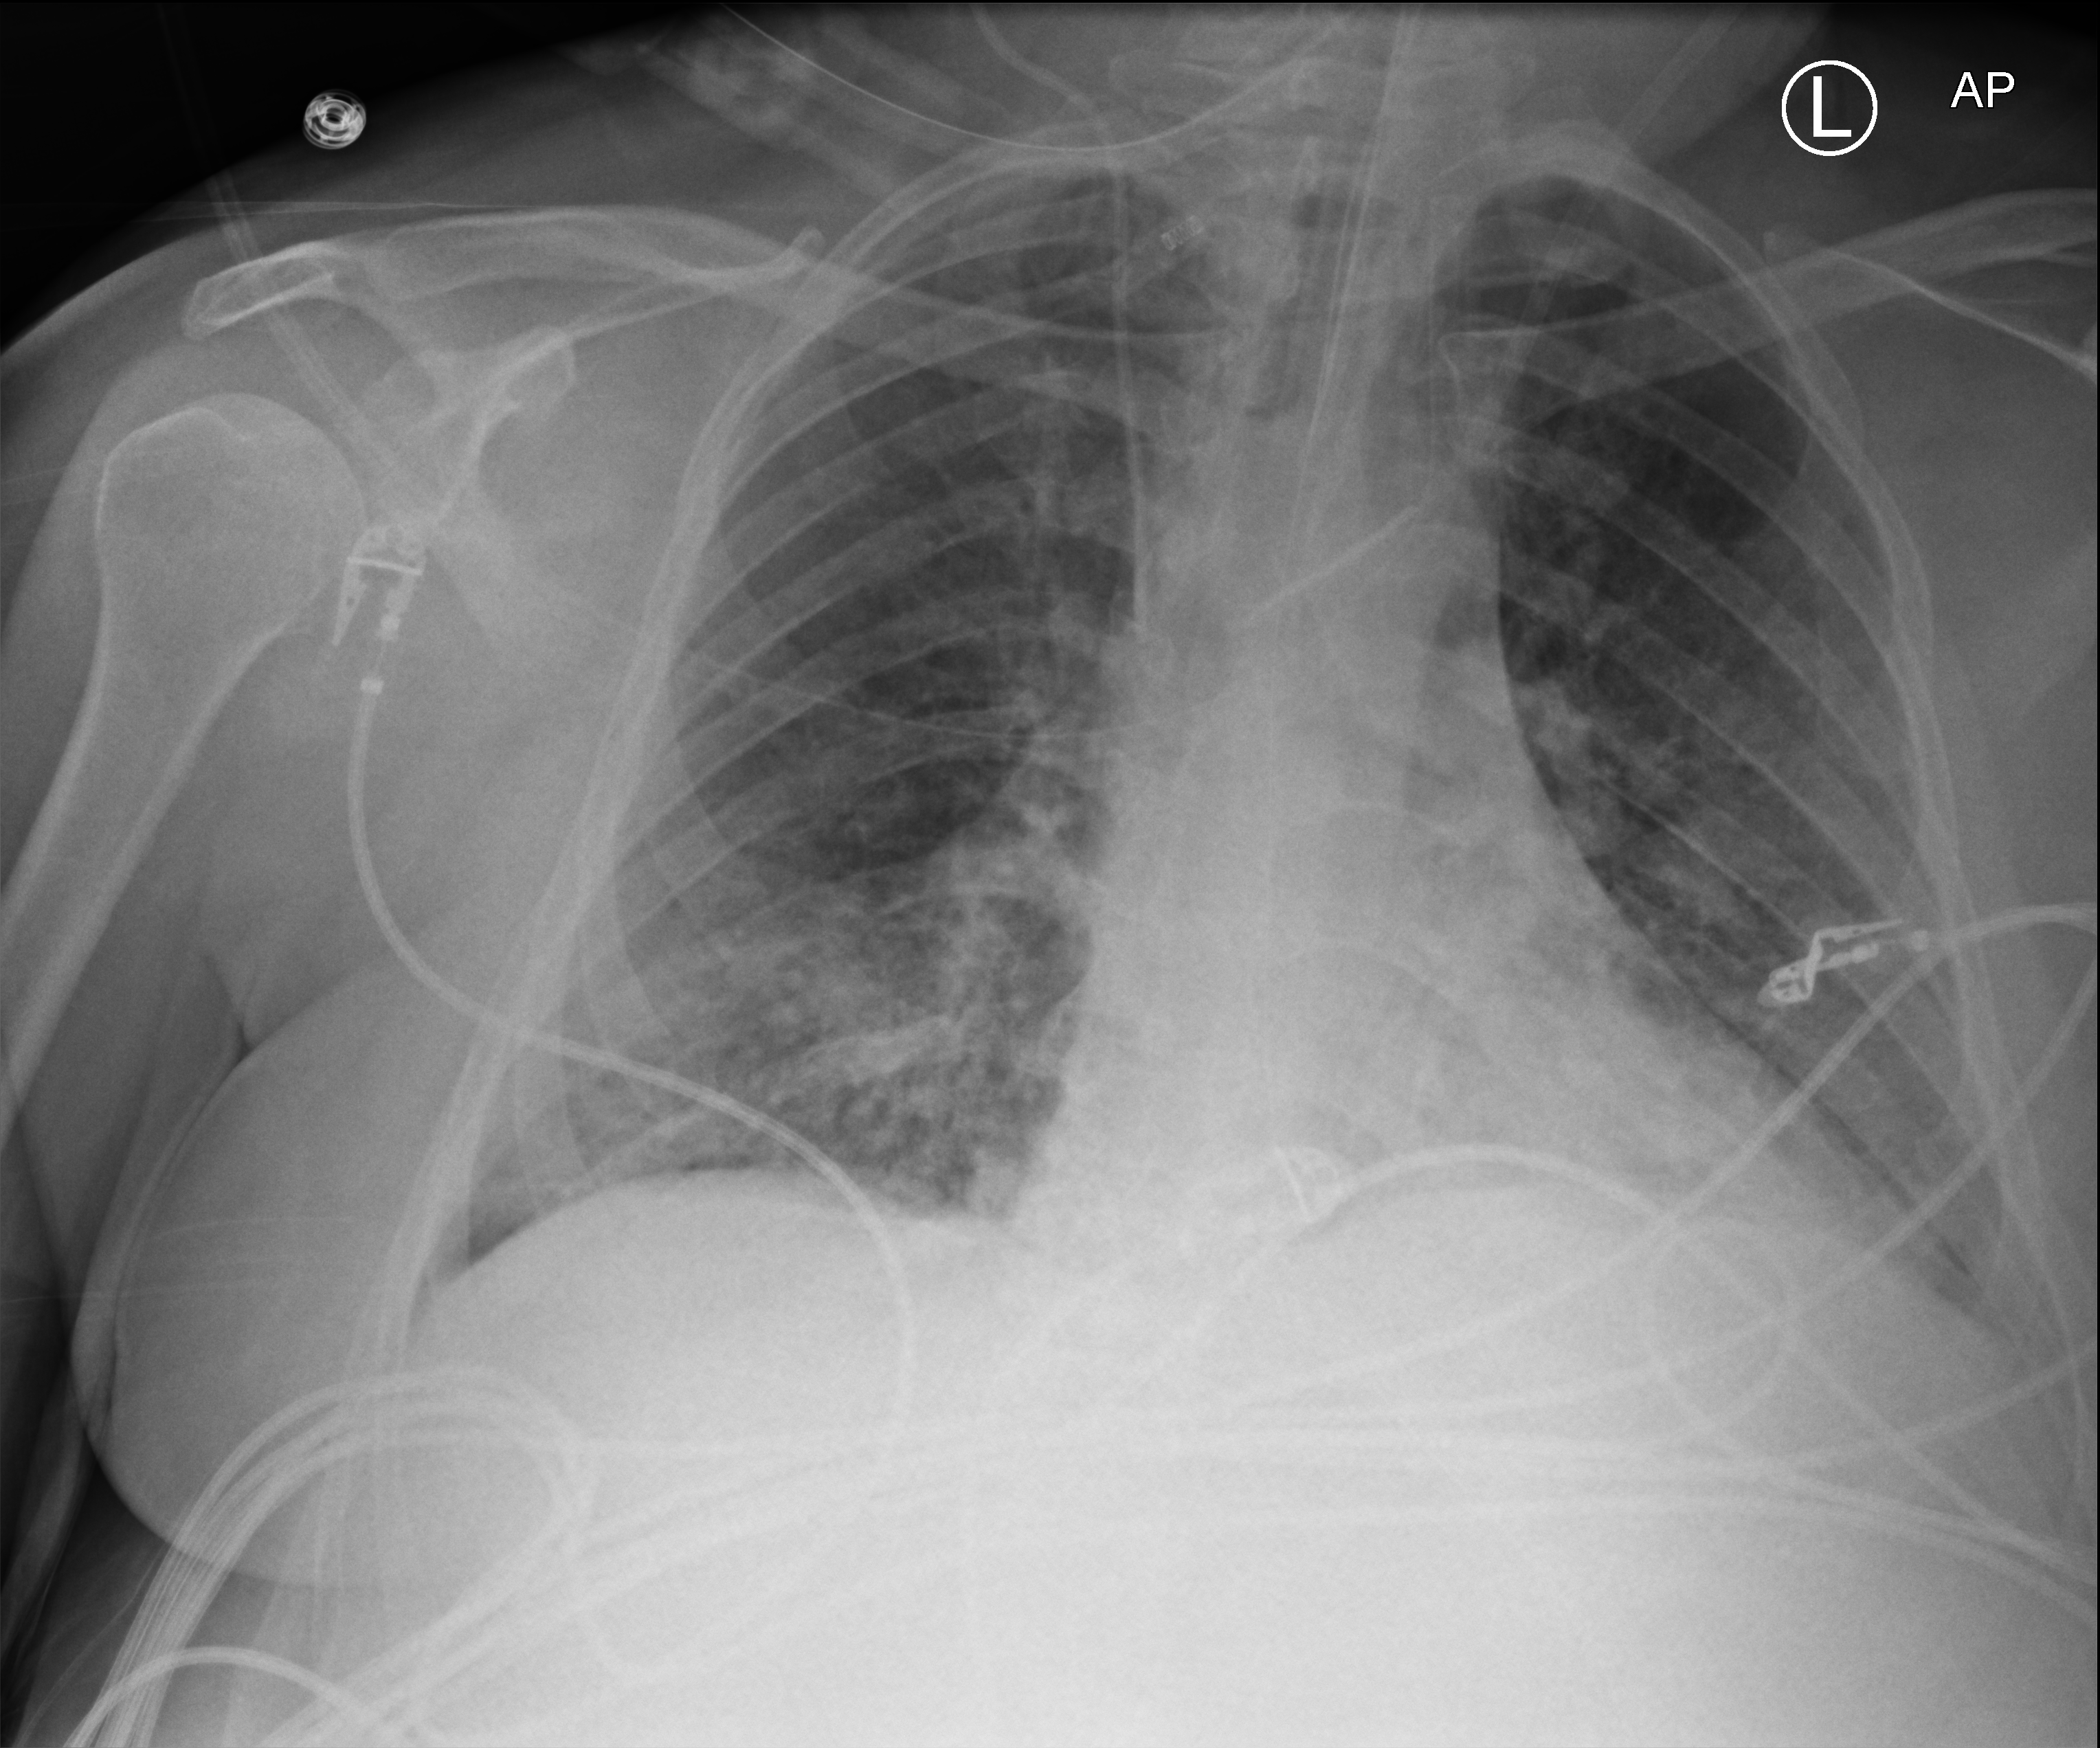
Bedside chest radiograph (computed radiography); anteroposterior (AP) projection. Male patient hospitalised with COVID-19, age 18–59 years.
From the hospital-stay record, not from the radiograph (when in the stay this image was taken is not recorded):
- admitted to intensive care during this hospital stay: yes
- other chronic lung disease (admission record): no
- mechanically ventilated during this hospital stay: yes